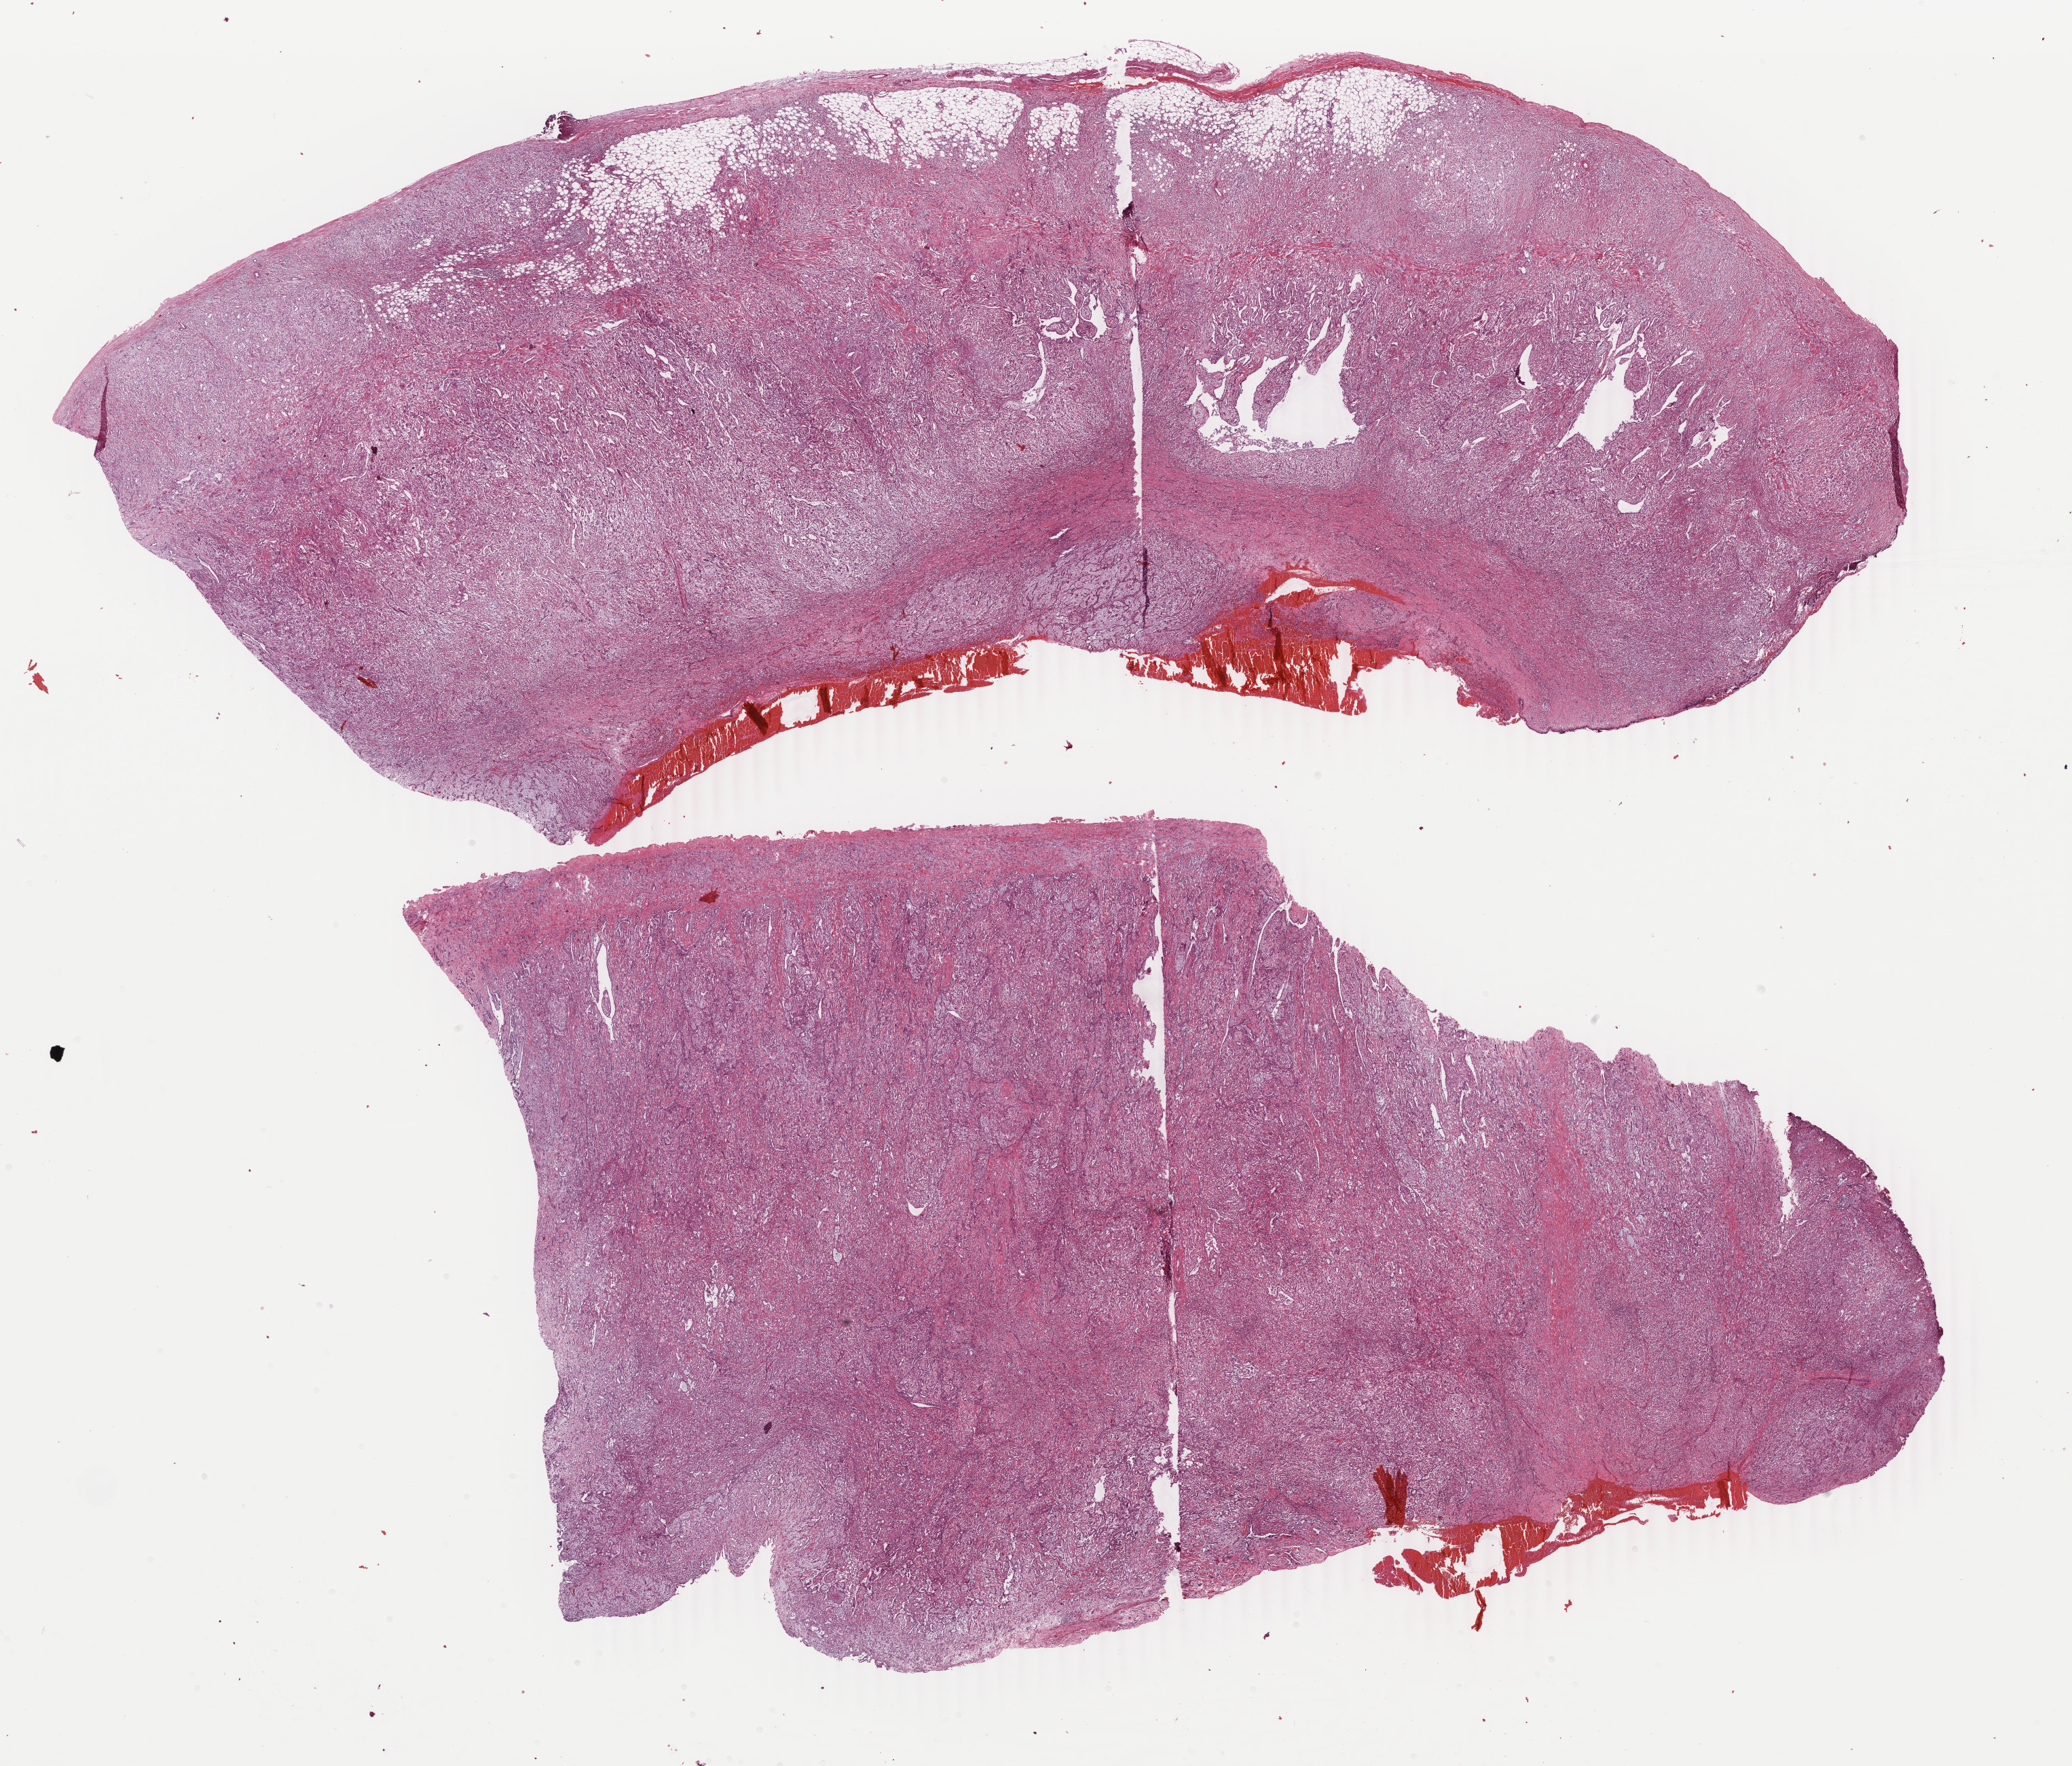
Digitized H&E tissue section (whole slide) — shown as a low-resolution overview of the whole scanned area (about 24.3 x 20.7 mm, from a 40x scan); FFPE section; primary tumour sample from the mesothelium. Female patient; age at initial diagnosis 66 years.
Laterality: right. AJCC pathologic stage: III (6th edition). Diagnosis: Mesothelioma, biphasic, malignant (pleura, NOS).